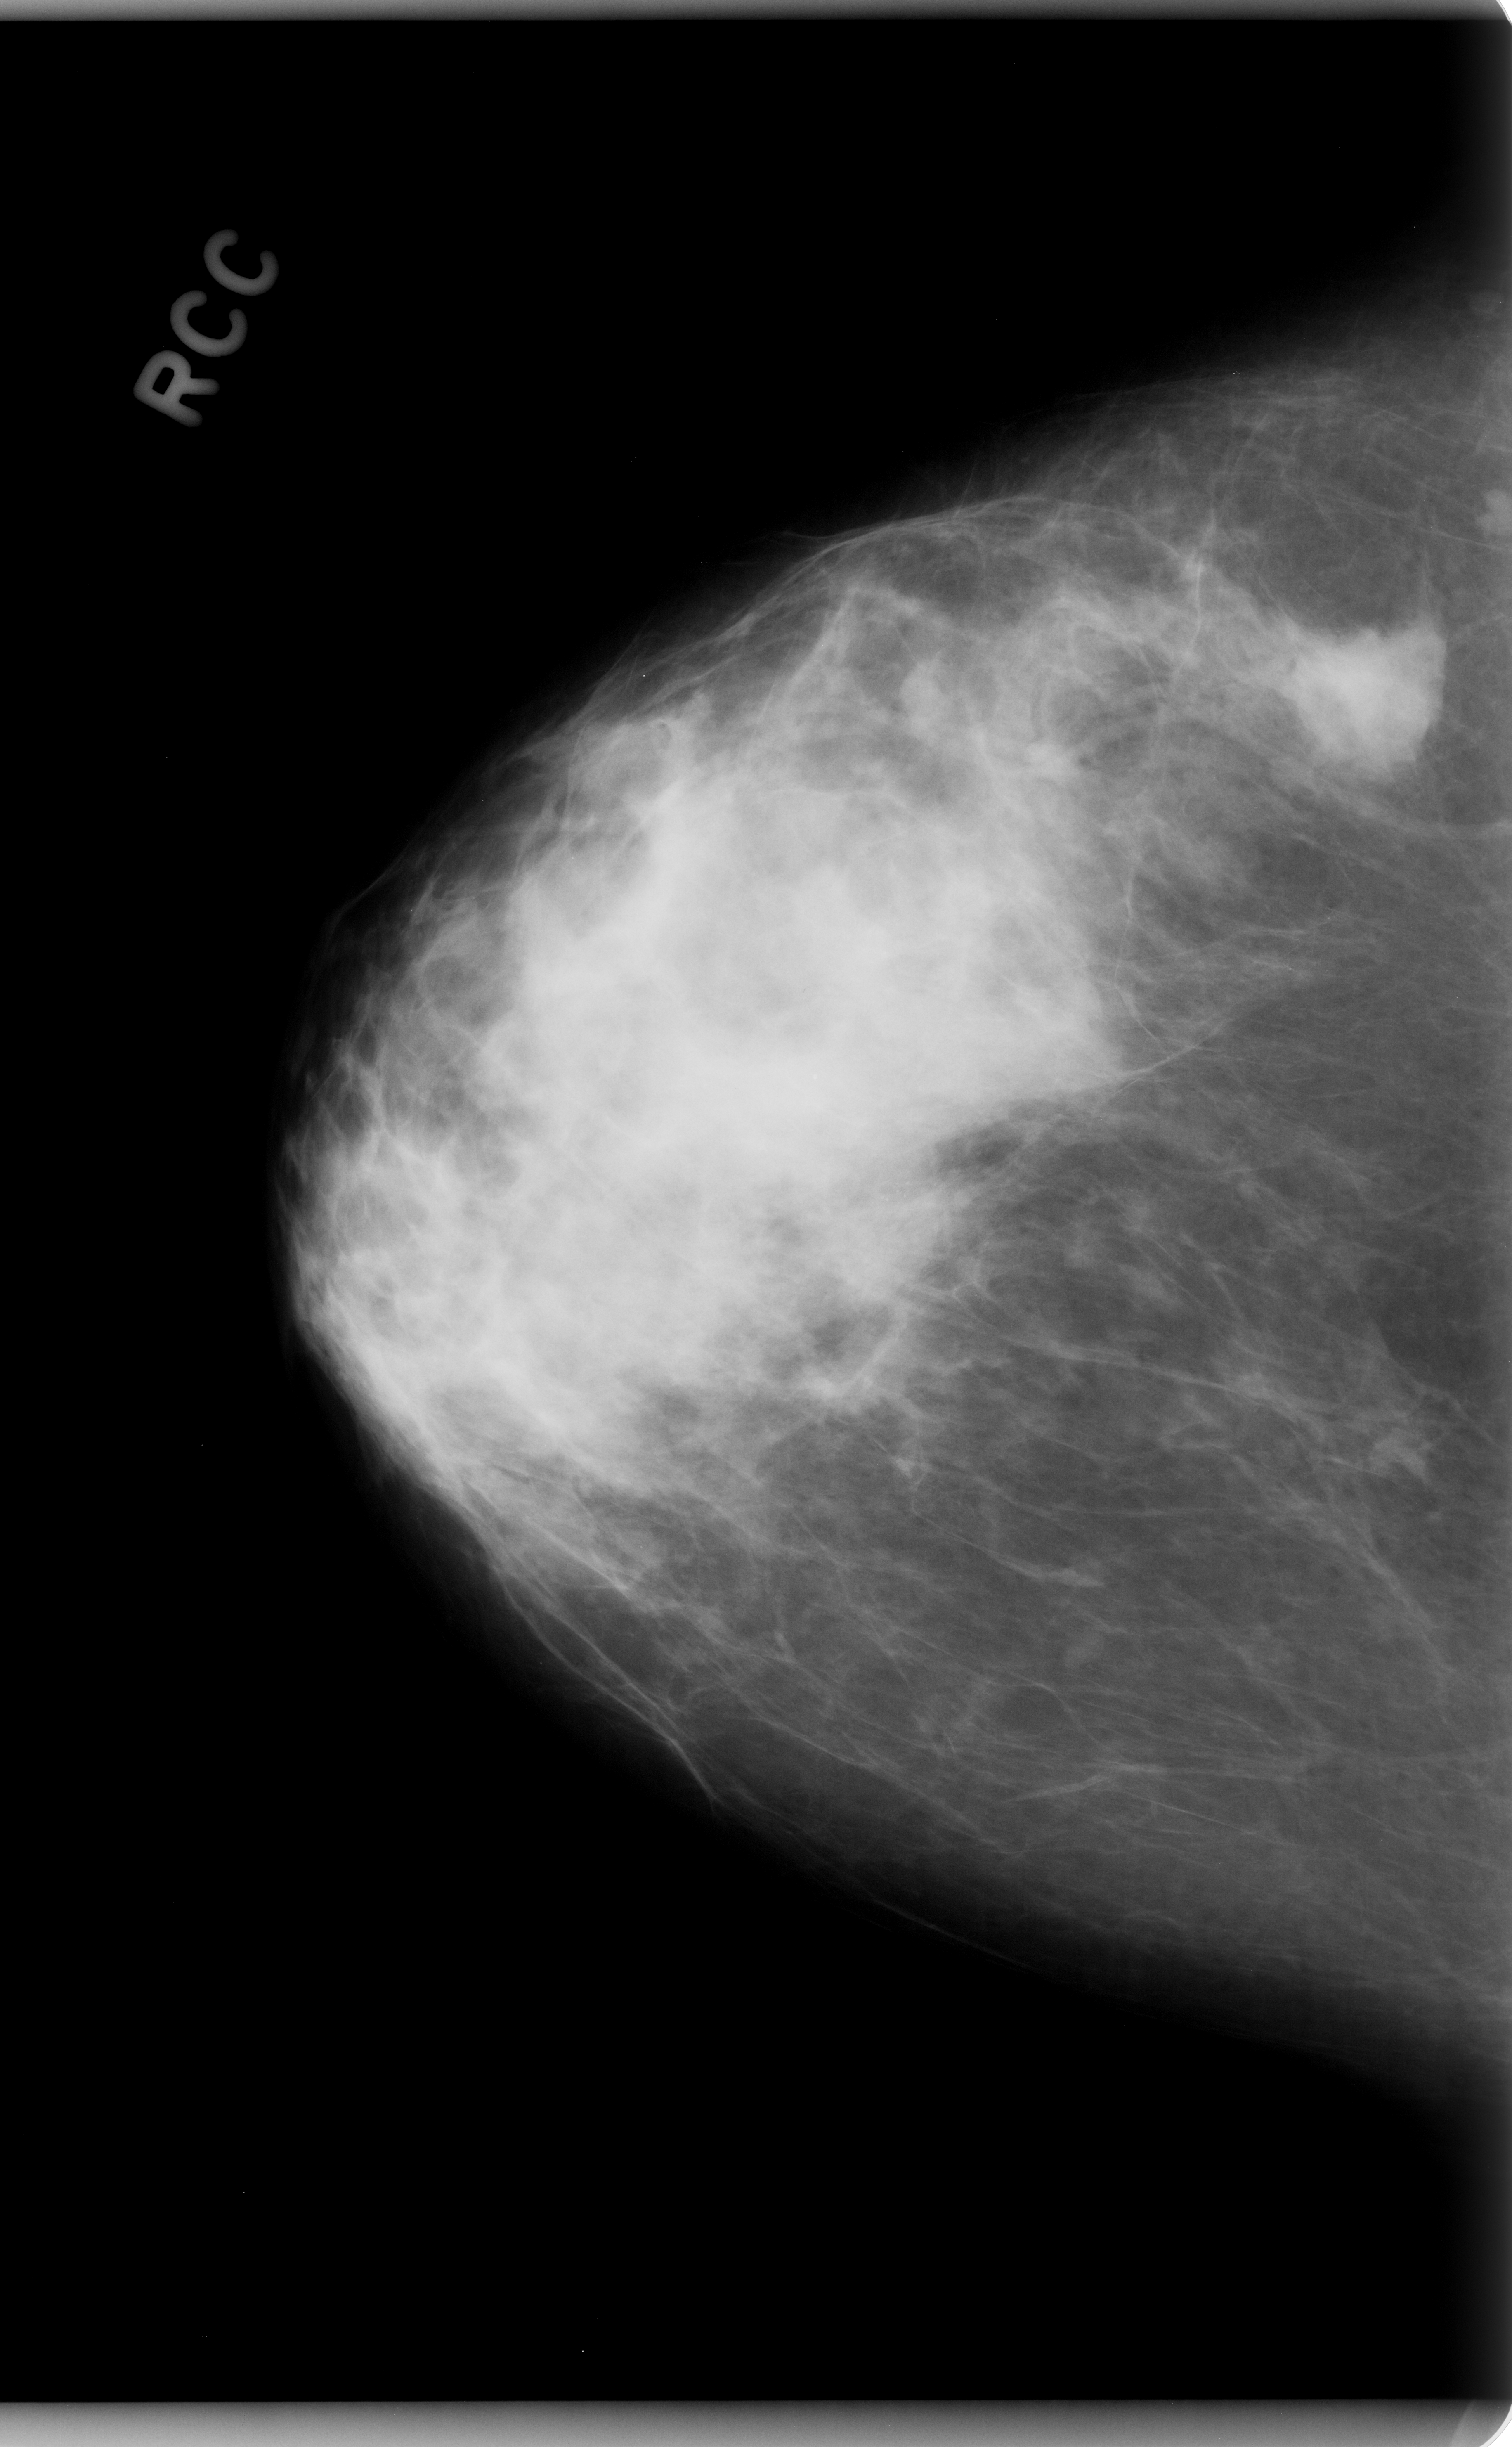
Scanned film-screen mammogram; right breast; CC view; BI-RADS breast density category 3 (scale 1–4); 1512 × 2447 image matrix.
Marked abnormalities (boxes around the expert regions of interest):
- mass, shape irregular, margins microlobulated; BI-RADS assessment category 5; pathology (as recorded): malignant: bounding box <1259,613,1417,779> (left, top, right, bottom; pixels)